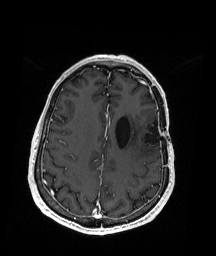
Brain MRI from a brain-tumour surgery series, one axial slice; position 63 of 192 along the scan axis; T1-weighted post-contrast; 216 × 256 image matrix, field of view 211 × 250 mm. Case-level facts recorded for this patient, not image findings: histopathology: Oligodendroglioma; WHO grade: 2; IDH mutation: yes; tumour location: Left Insular.
Outlined on this slice (manually delineated by an expert):
- previous resection cavity: bounding box <132,124,163,147> (left, top, right, bottom; pixels)